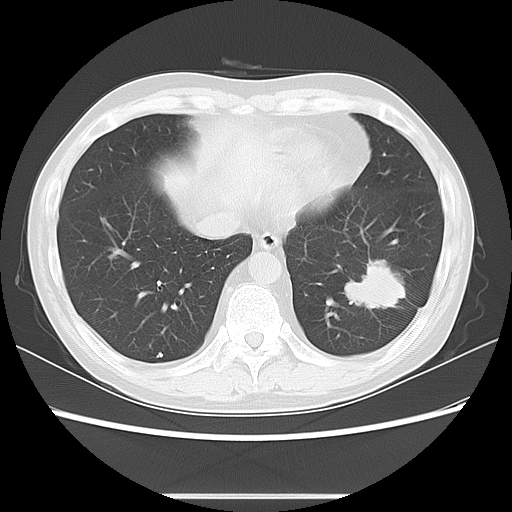
Chest CT, one axial slice; position 23 of 63 along the scan axis; reconstruction kernel LUNG; lung window (W 1500 / L -600 HU); 5 mm slice thickness; 512 × 512 image matrix, field of view 347 × 347 mm. Male patient, age 49 years. Case-level facts recorded for this patient, not image findings: clinical TNM (as recorded): T3 N0 M0.
Outlined on this slice (rectangle marked by the reading radiologist):
- lung tumour (recorded histology: squamous cell carcinoma): bounding box (x1, y1, x2, y2) in pixels: (341, 254, 419, 324)